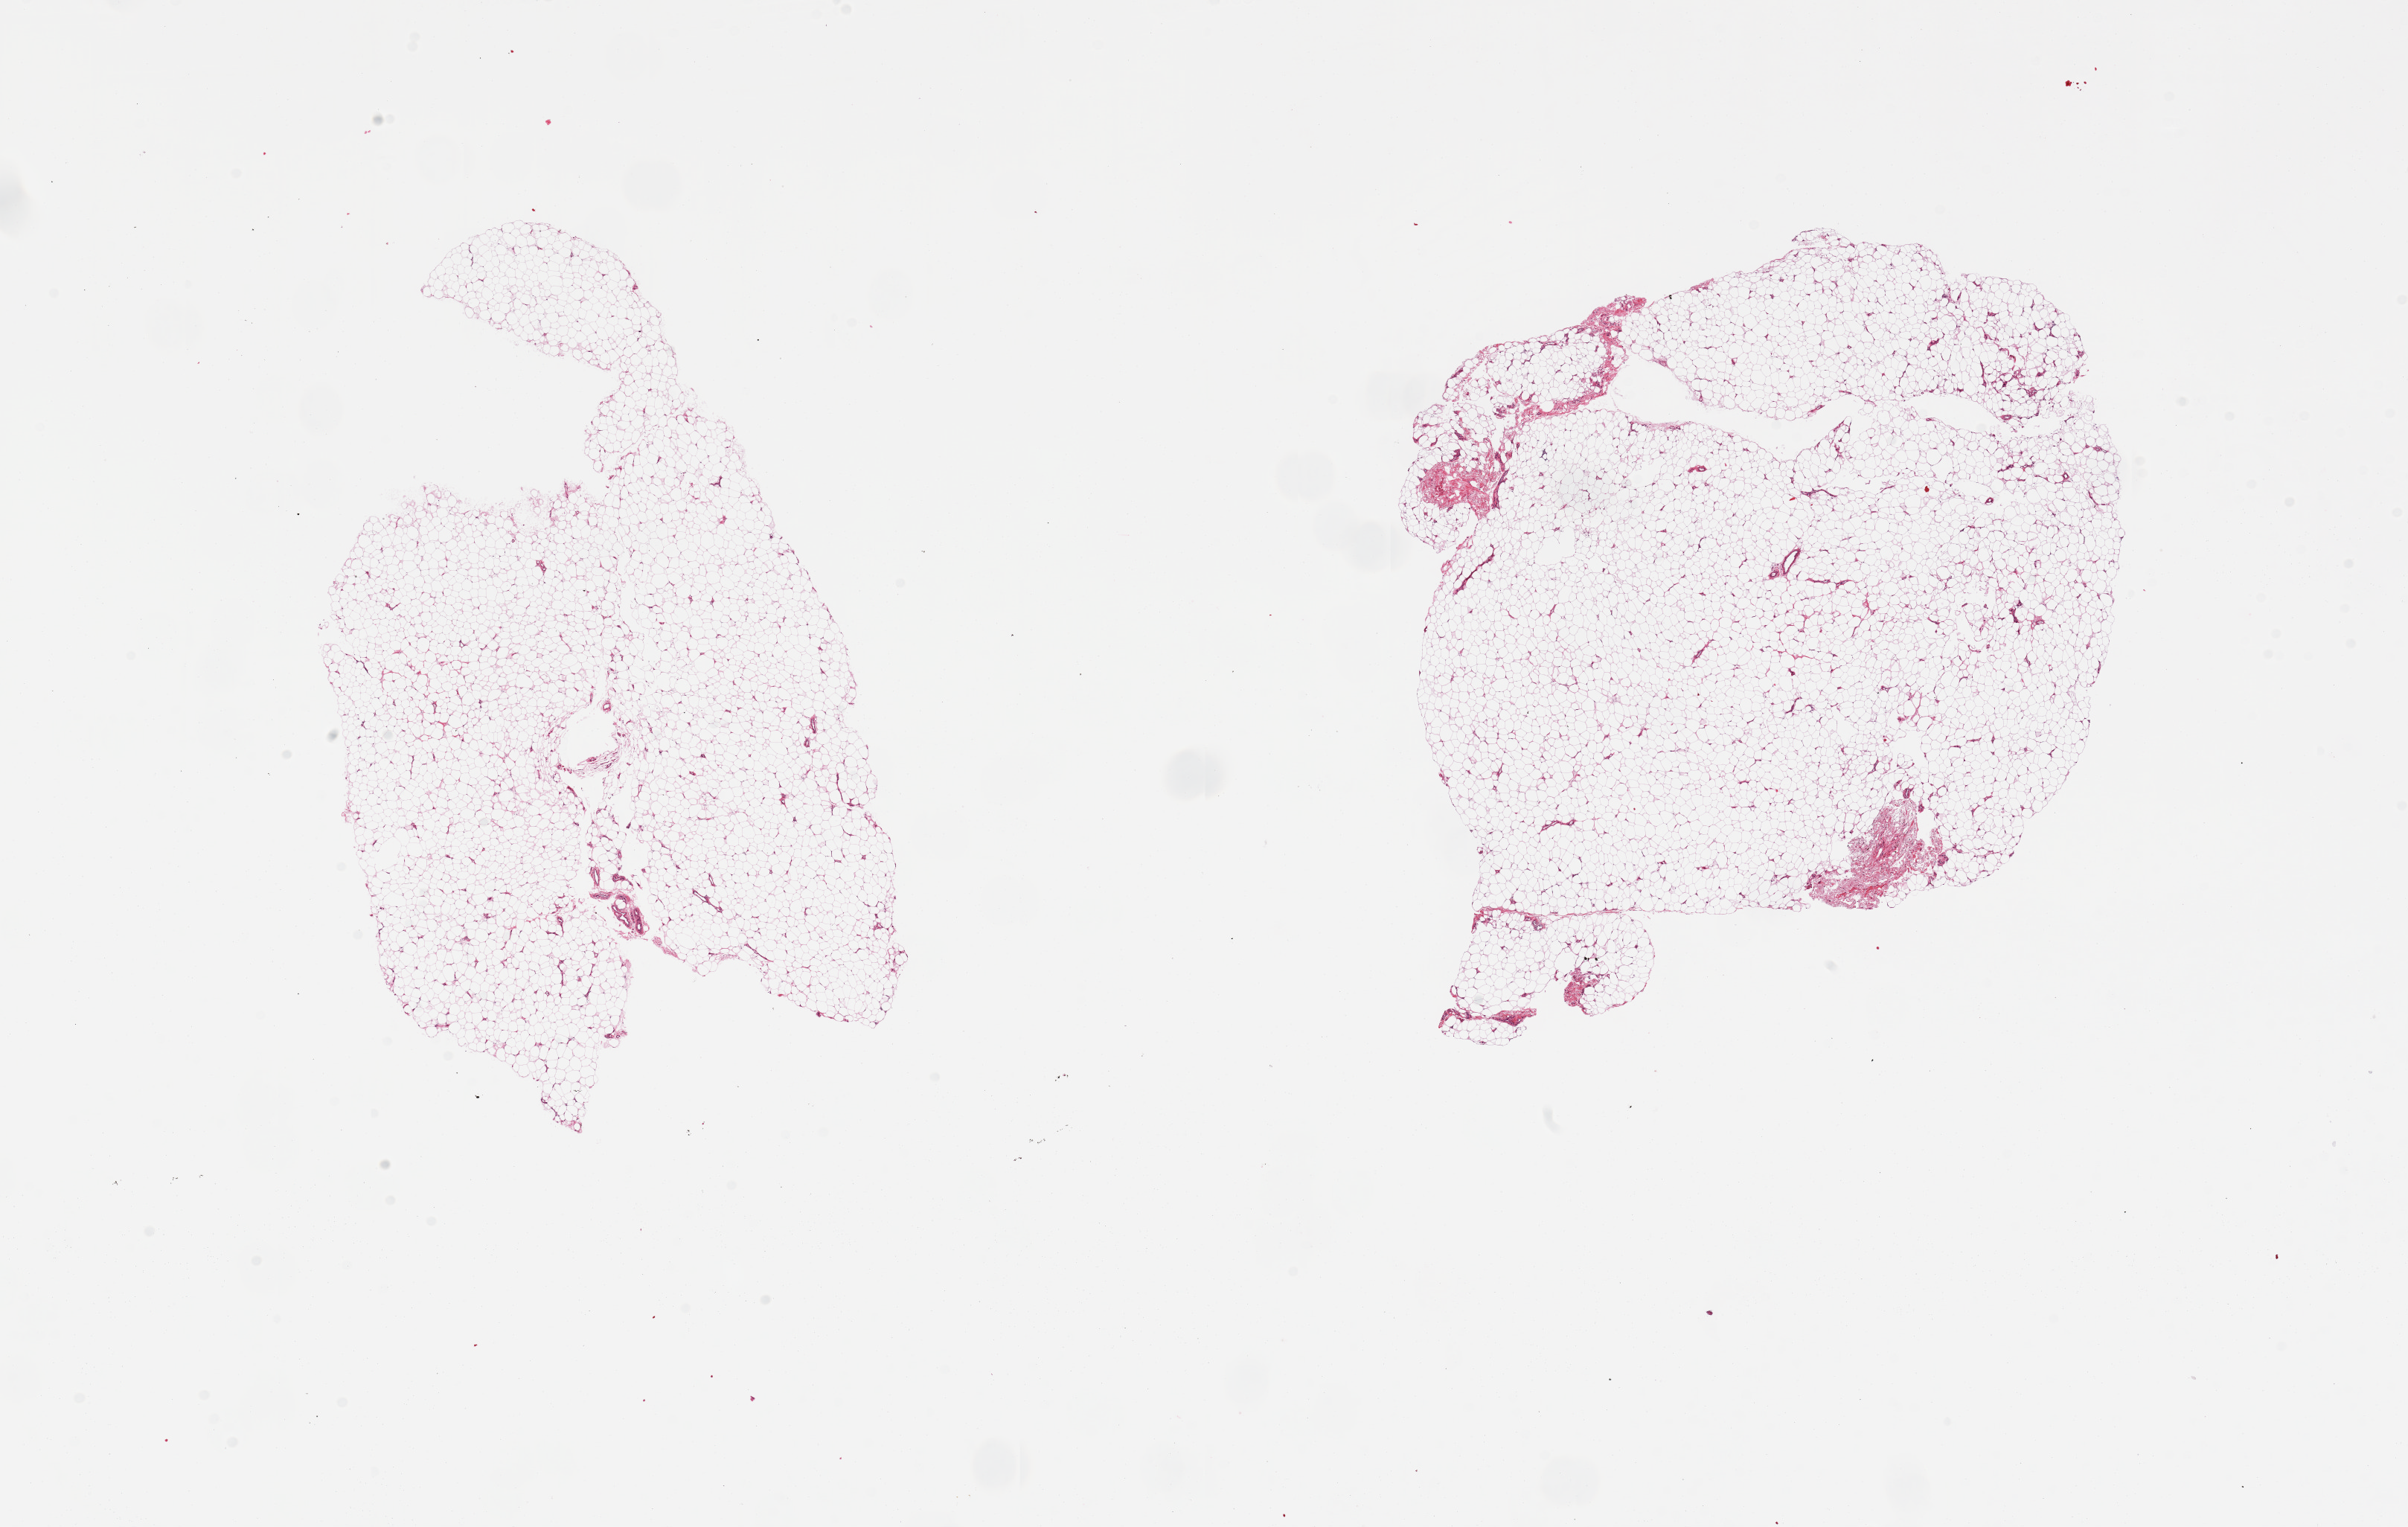
Hematoxylin and eosin (H&E) whole-slide image — shown as a low-resolution overview of the whole scanned area (about 25.6 x 16.2 mm), PAXgene-fixed paraffin-embedded (PFPE) section, section of adipose tissue (target tissue), tissue donor sample. Donor sex: female.
Reviewer comment on this tissue sample: 2 pieces.